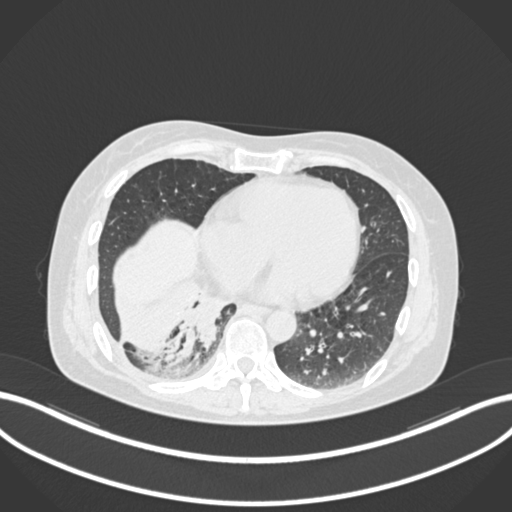
Chest CT, one axial slice; slice 48 of 168 in the series (ordered by position); reconstruction kernel B30f; 120 kVp; lung window (W 1500 / L -600 HU); 512 × 512 image matrix, field of view 400 × 400 mm. Patient: female, 63 years. From the clinical record (not read from this slice): clinical TNM (as recorded): T1c N0 M0.
Outlined on this slice (rectangle marked by the reading radiologist):
- lung tumour (recorded histology: adenocarcinoma): bounding box (x1, y1, x2, y2) in pixels: (176, 296, 227, 357)